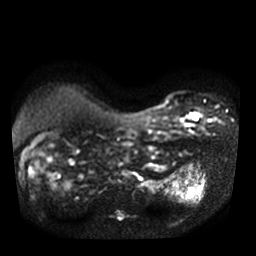
Breast MRI, one axial slice; position 14 of 36 along the scan axis; diffusion-weighted series; image 2 of 4 stored at this slice position (different b-values; order by instance number); 3 T; 256 × 256 image matrix. Female patient.
Structures marked on this image (manually delineated by an expert):
- tumour on diffusion-weighted imaging: box from (x=186, y=113) to (x=197, y=119) px